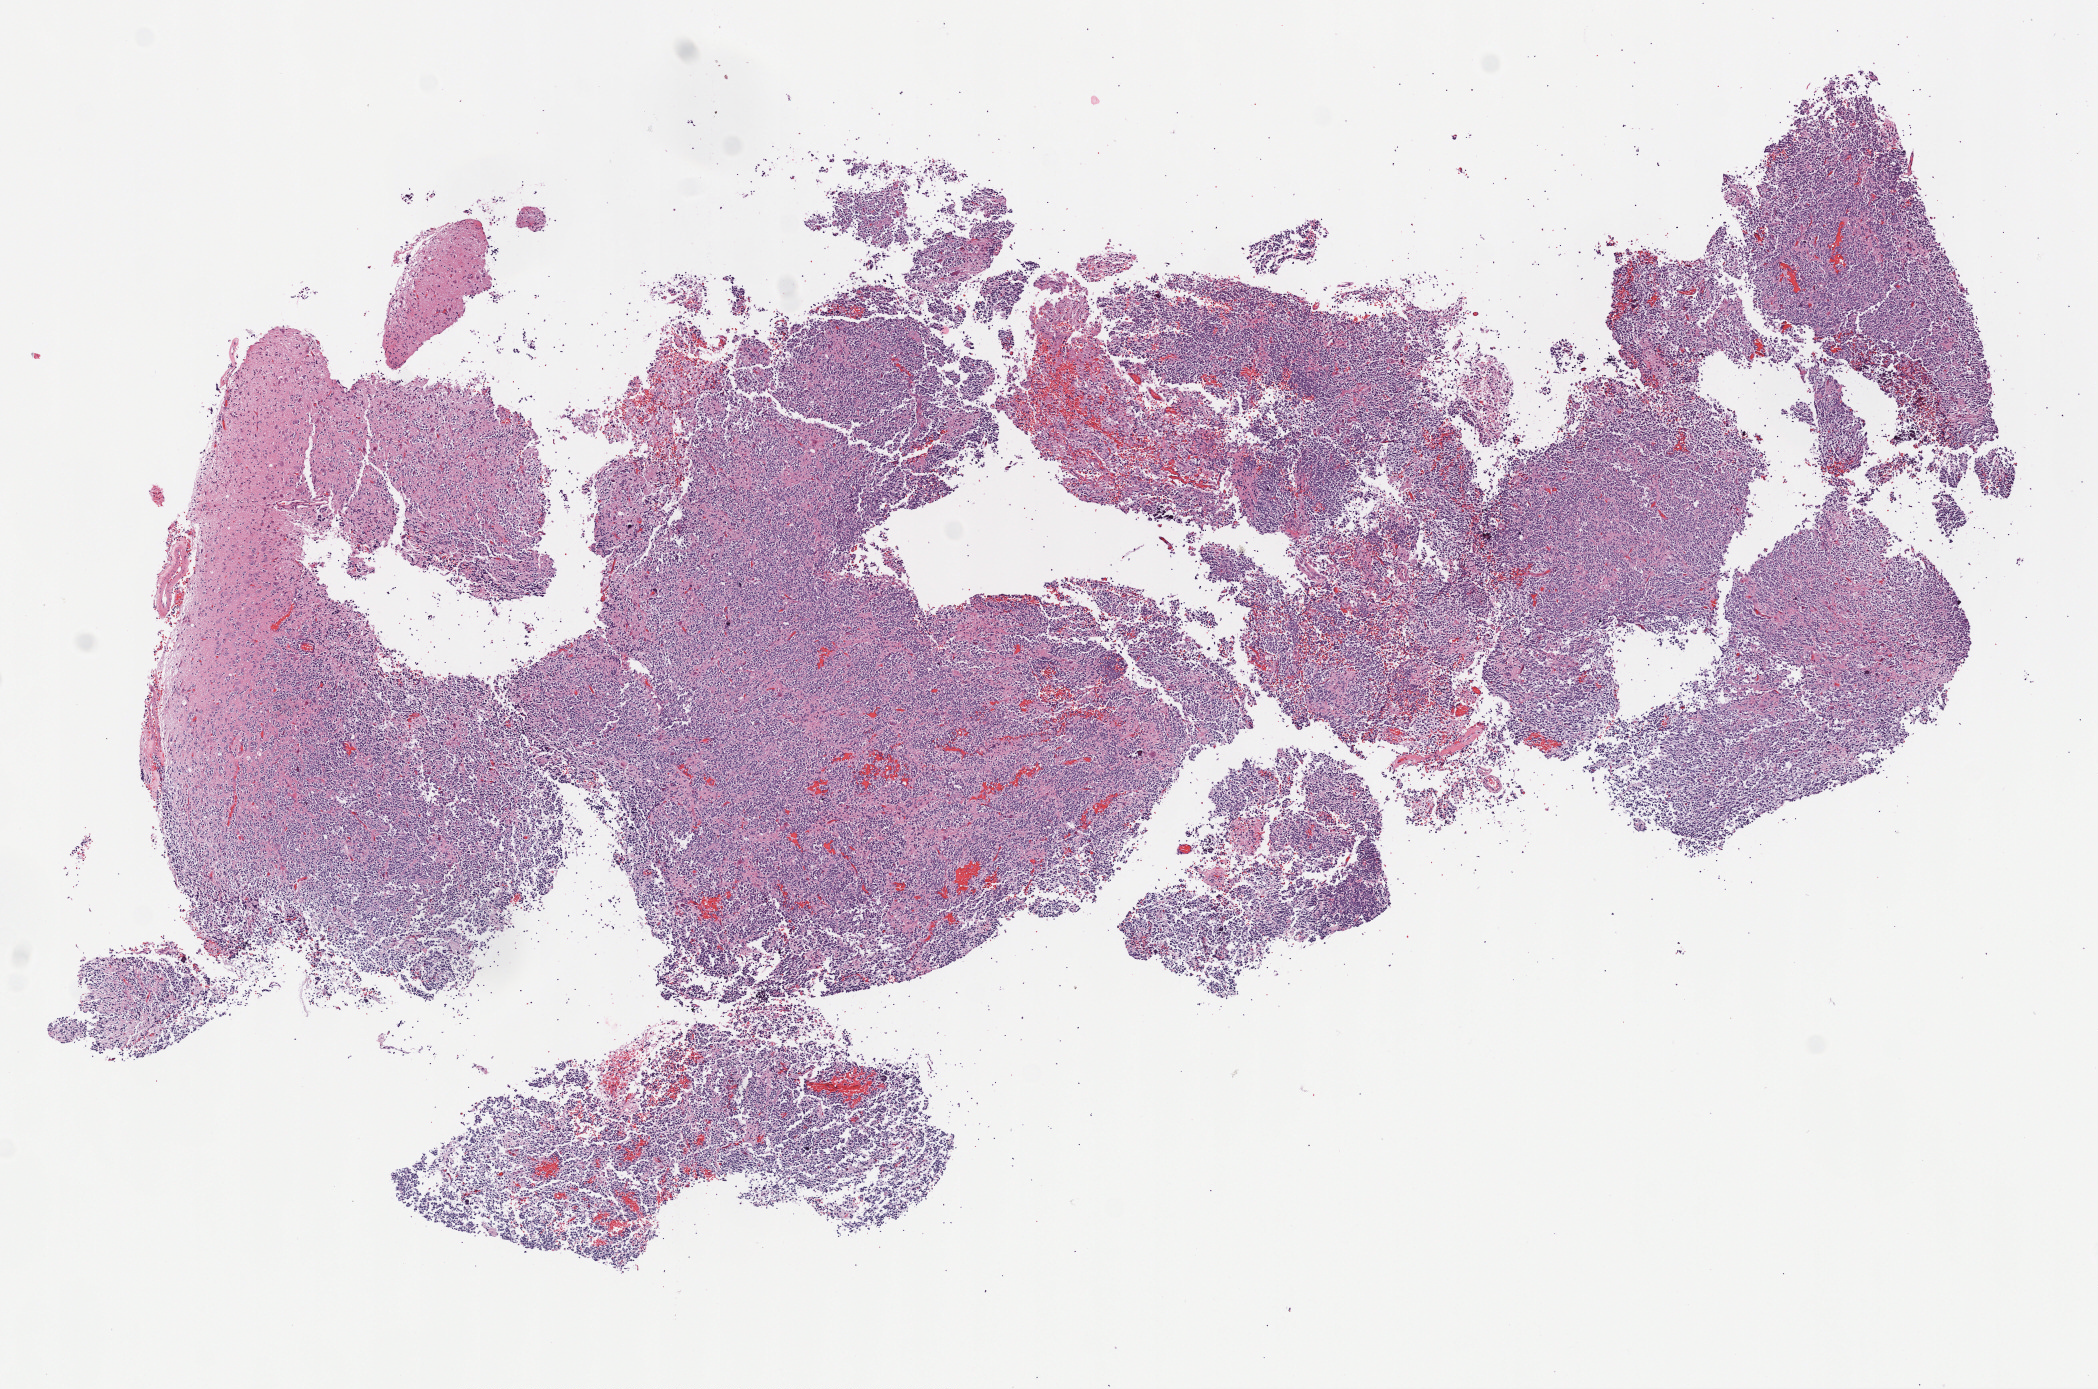
Digitized H&E-stained tissue section (whole slide) — shown as a low-resolution overview of the whole scanned area (about 8.5 x 5.6 mm, slide scanned at 40x); formalin-fixed paraffin-embedded (FFPE) diagnostic section; sample: primary tumour, brain. Female patient; age at initial diagnosis 55 years.
Histologic diagnosis: Oligodendroglioma, anaplastic (cerebrum).